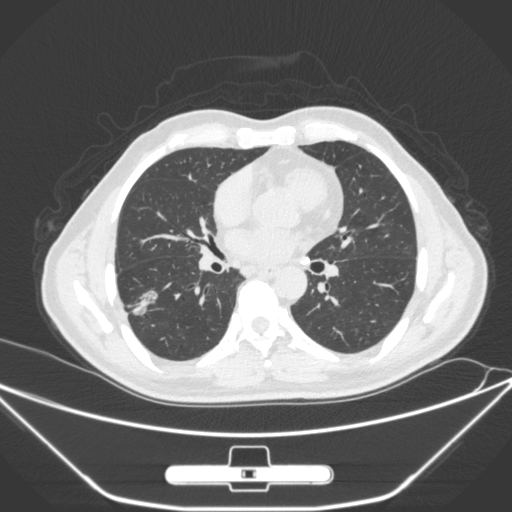
Chest CT, one axial slice; slice 143 of 310 in the series (ordered by position); lung window (W 1500 / L -600 HU); 512 × 512 image matrix, field of view 398 × 398 mm. Male patient, age 71 years. From the clinical record (not read from this slice): clinical TNM (as recorded): T1c N0 M0; histopathological grade: G2.
Annotated regions visible in this slice (rectangle marked by the reading radiologist):
- lung tumour (recorded histology: adenocarcinoma): box from (x=127, y=285) to (x=166, y=317) px